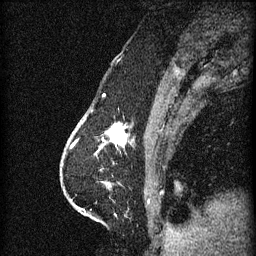
Breast MRI (dynamic contrast-enhanced), one sagittal slice; position 21 of 60 along the scan axis; 3 images stored at this slice position (order not interpretable as contrast timing); 1.5 T; TE 4.2 ms, TR 11 ms; 256 × 256 image matrix. Female patient, age 63 years.
Outlined on this slice (semi-automatically segmented with operator editing):
- analysis volume of interest (the breast-tissue region the enhancement analysis was run in; not a lesion): box from (x=86, y=118) to (x=133, y=153) px
- tumour enhancement mask (voxels above the 70 % enhancement threshold inside the analysis volume of interest): (x=104, y=126)–(x=127, y=147)